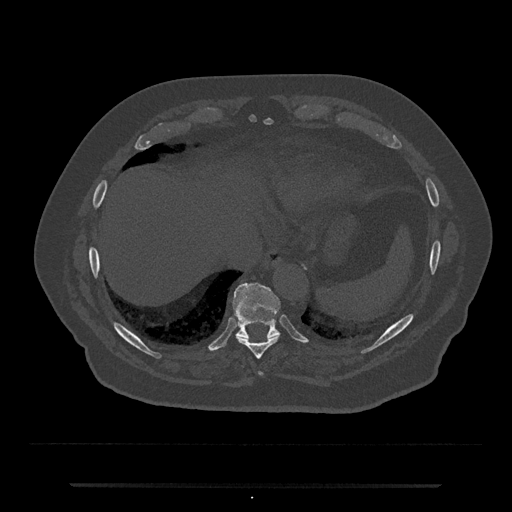
CT including the spine, one axial slice. Slice 737 of 797 in the series (ordered by position). Reconstruction kernel Br40s/3. Bone window (W 1800 / L 400 HU). 512 × 512 image matrix. Male patient, age 80 years. Case-level facts recorded for this patient, not image findings: primary cancer: prostate; vertebrae with lytic lesions (as recorded): L1, T11.
Structures marked on this image (semi-automatically segmented with operator editing):
- T10 vertebra: box from (x=233, y=283) to (x=280, y=338) px
- T8 vertebra: (x=259, y=373)–(x=262, y=376)
- T9 vertebra: (x=236, y=335)–(x=280, y=359)